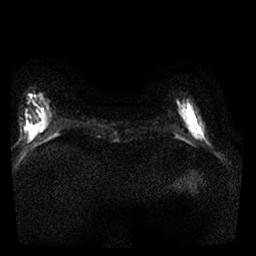
Breast MRI, one axial slice. Position 5 of 25 along the scan axis. Diffusion-weighted series; image 2 of 4 stored at this slice position (different b-values; order by instance number). 1.5 T. 4 mm slice thickness. 256 × 256 image matrix. Female patient.
Structures marked on this image (manually delineated by an expert):
- tumour on diffusion-weighted imaging: box from (x=177, y=95) to (x=205, y=142) px